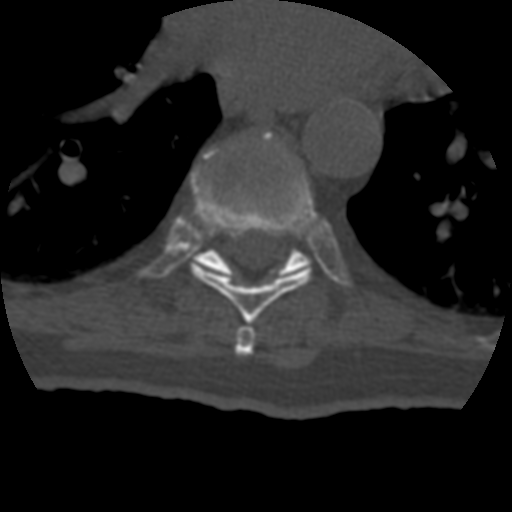
CT including the spine, one axial slice. Slice 253 of 399 in the series (ordered by position). 120 kVp. Bone window (W 1800 / L 400 HU). 1.25 mm slice thickness. 512 × 512 image matrix, field of view 160 × 160 mm. Patient age 69 years. From the clinical record (not read from this slice): primary cancer: prostate.
Outlined on this slice (semi-automatic segmentation, software-assisted and operator-edited):
- T7 vertebra: bounding box (x1, y1, x2, y2) in pixels: (235, 325, 256, 356)
- T8 vertebra: (191, 154, 317, 323)
- T9 vertebra: (197, 131, 308, 277)